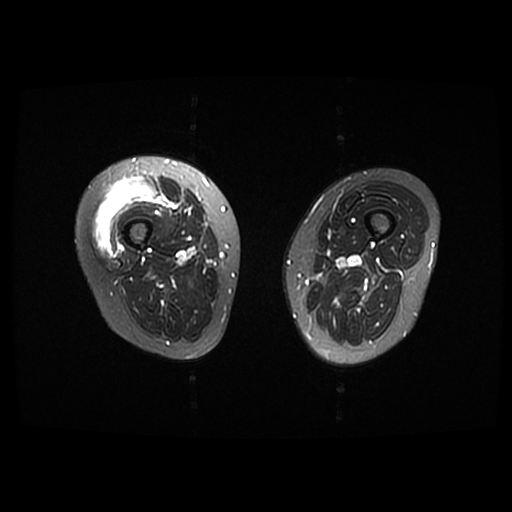
MRI of an extremity soft-tissue mass, one axial slice; position 8 of 42 along the scan axis; T2-weighted fat-saturated; 6 mm slice thickness; 512 × 512 image matrix, field of view 440 × 440 mm. Female patient. From the clinical record (not read from this slice): histological type: pleiomorphic undifferentiated sarcoma; grade: high; site of the primary tumour: right quadricep.
Structures marked on this image (outlined manually by an expert reader):
- gross tumour volume including surrounding oedema: bounding box <94,175,157,256> (left, top, right, bottom; pixels)